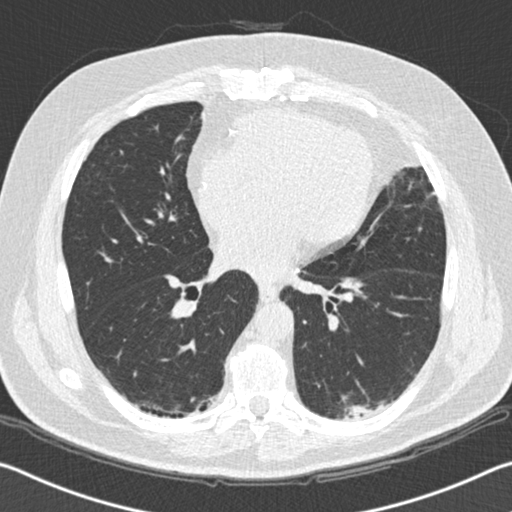
Low-dose screening chest CT, one axial slice. Slice 83 of 172 in the series (ordered by position). 120 kVp. Lung window (W 1500 / L -600 HU). 2 mm slice thickness. 512 × 512 image matrix.
Outlined on this slice (outlined manually by an expert reader):
- lesion 1 (tumor, lower lobe of left lung): box from (x=343, y=404) to (x=374, y=420) px